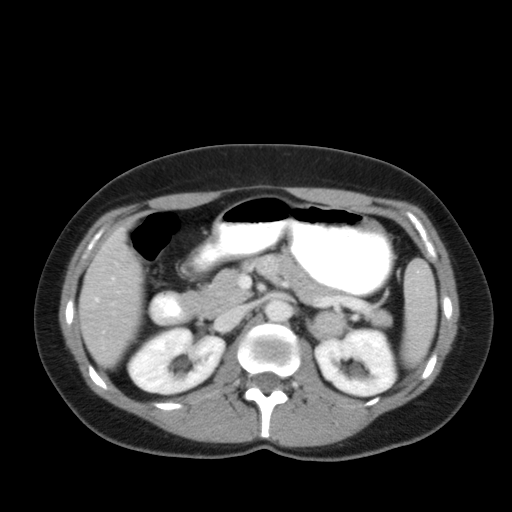
Contrast-enhanced abdominal CT, one axial slice. Position 29 of 92 along the scan axis. Reconstruction kernel FC12. 120 kVp. Intravenous contrast given. Soft-tissue window (W 400 / L 40 HU). 5 mm slice thickness. 512 × 512 image matrix. Patient: female, 35 years. Case-level facts recorded for this patient, not image findings: diagnosis: adrenocortical carcinoma; tumour side: left adrenal; tumour size at pathology: 6.6 cm; Ki-67 index: 5 %; stage (as recorded): 2.
Structures marked on this image (semi-automatic segmentation, software-assisted and operator-edited):
- mass: bounding box (x1, y1, x2, y2) in pixels: (312, 312, 344, 338)